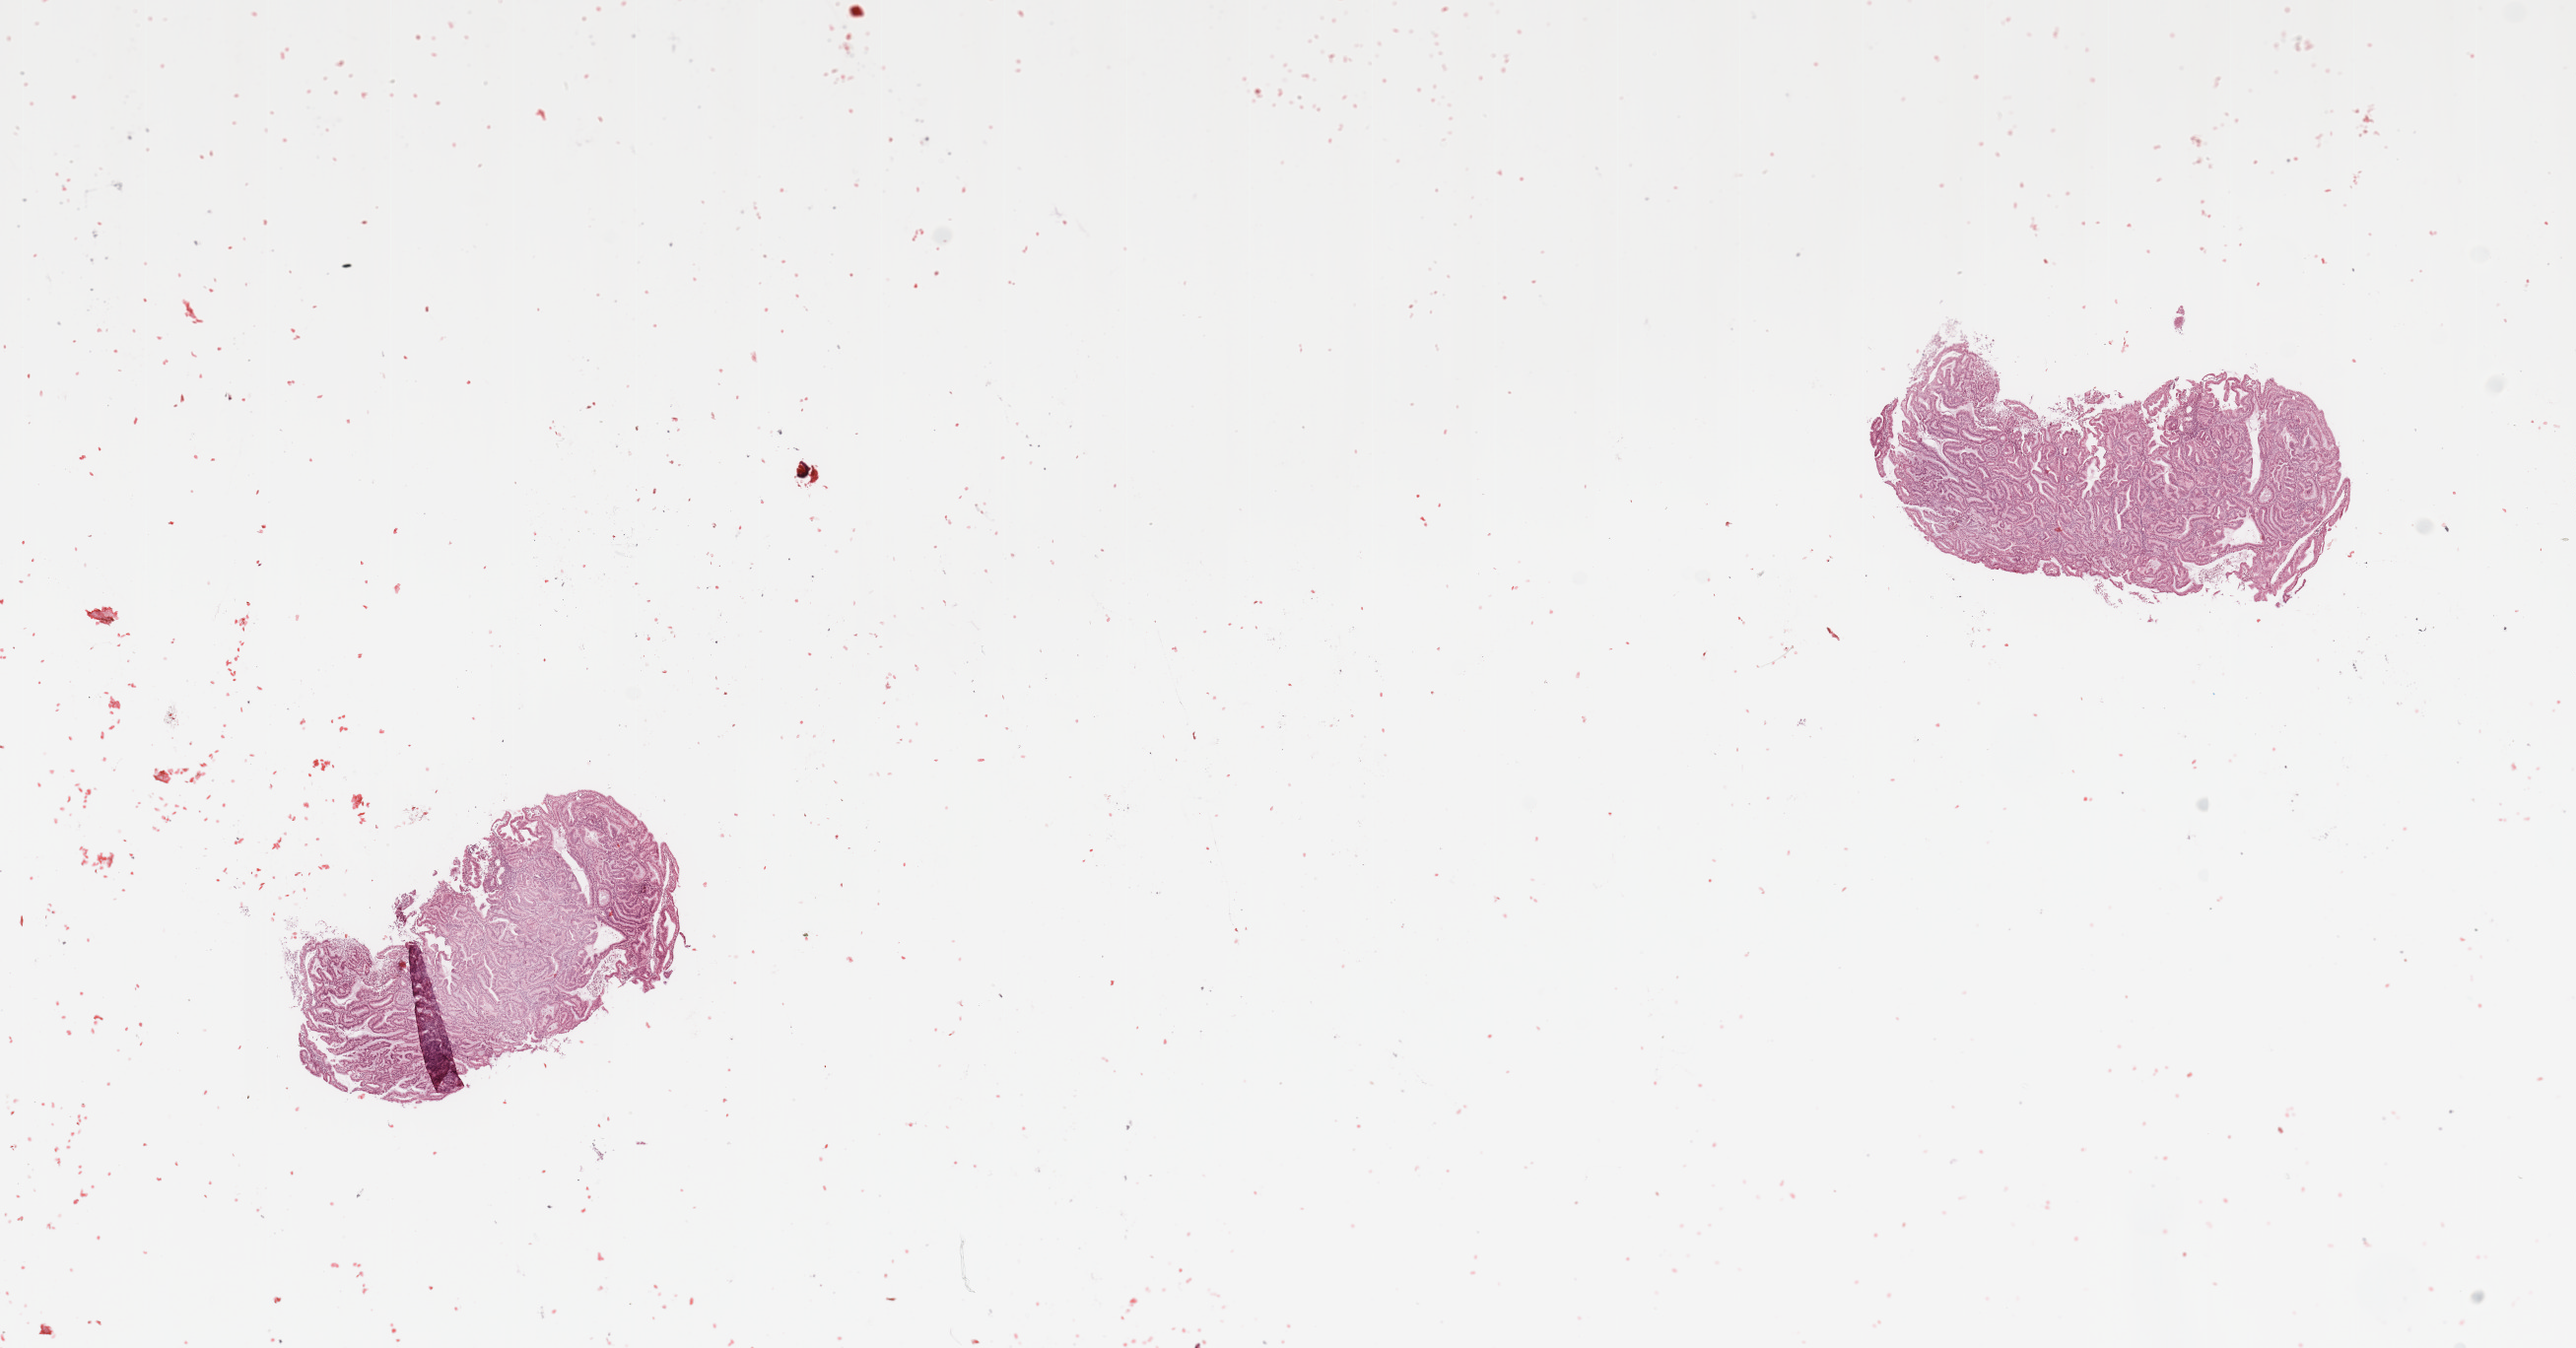
Whole-slide histology image, H&E — a low-resolution overview of the entire scanned area, about 20.7 x 10.8 mm; tumour tissue sample, sampled site: uterus. Patient: female, age 67 years. Histologic grade: G1 (well differentiated). Pathologist review of this section (percent, as recorded): tumour nuclei 90%, necrosis 0%.
AJCC pathologic stage: I. Histologic diagnosis: Endometrioid adenocarcinoma, NOS. Primary tumour site (as recorded): posterior endometrium.